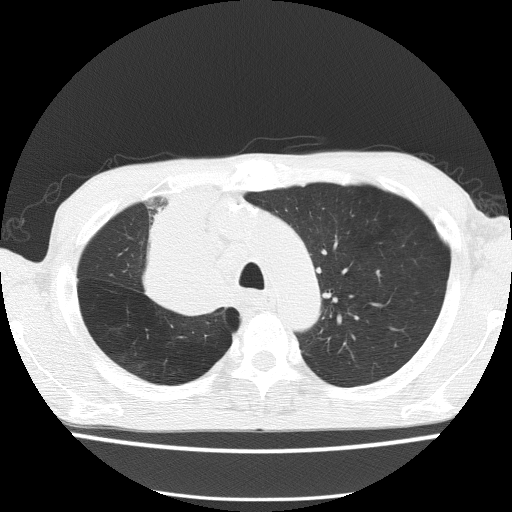
Low-dose screening chest CT, one axial slice. Position 113 of 150 along the scan axis. 120 kVp. Lung window (W 1500 / L -600 HU). 2 mm slice thickness. 512 × 512 image matrix, field of view 336 × 336 mm.
Outlined on this slice (manually delineated by an expert):
- lesion 1 (tumor, hilum of right lung): bounding box [x1, y1, x2, y2] px = [146, 188, 217, 315]